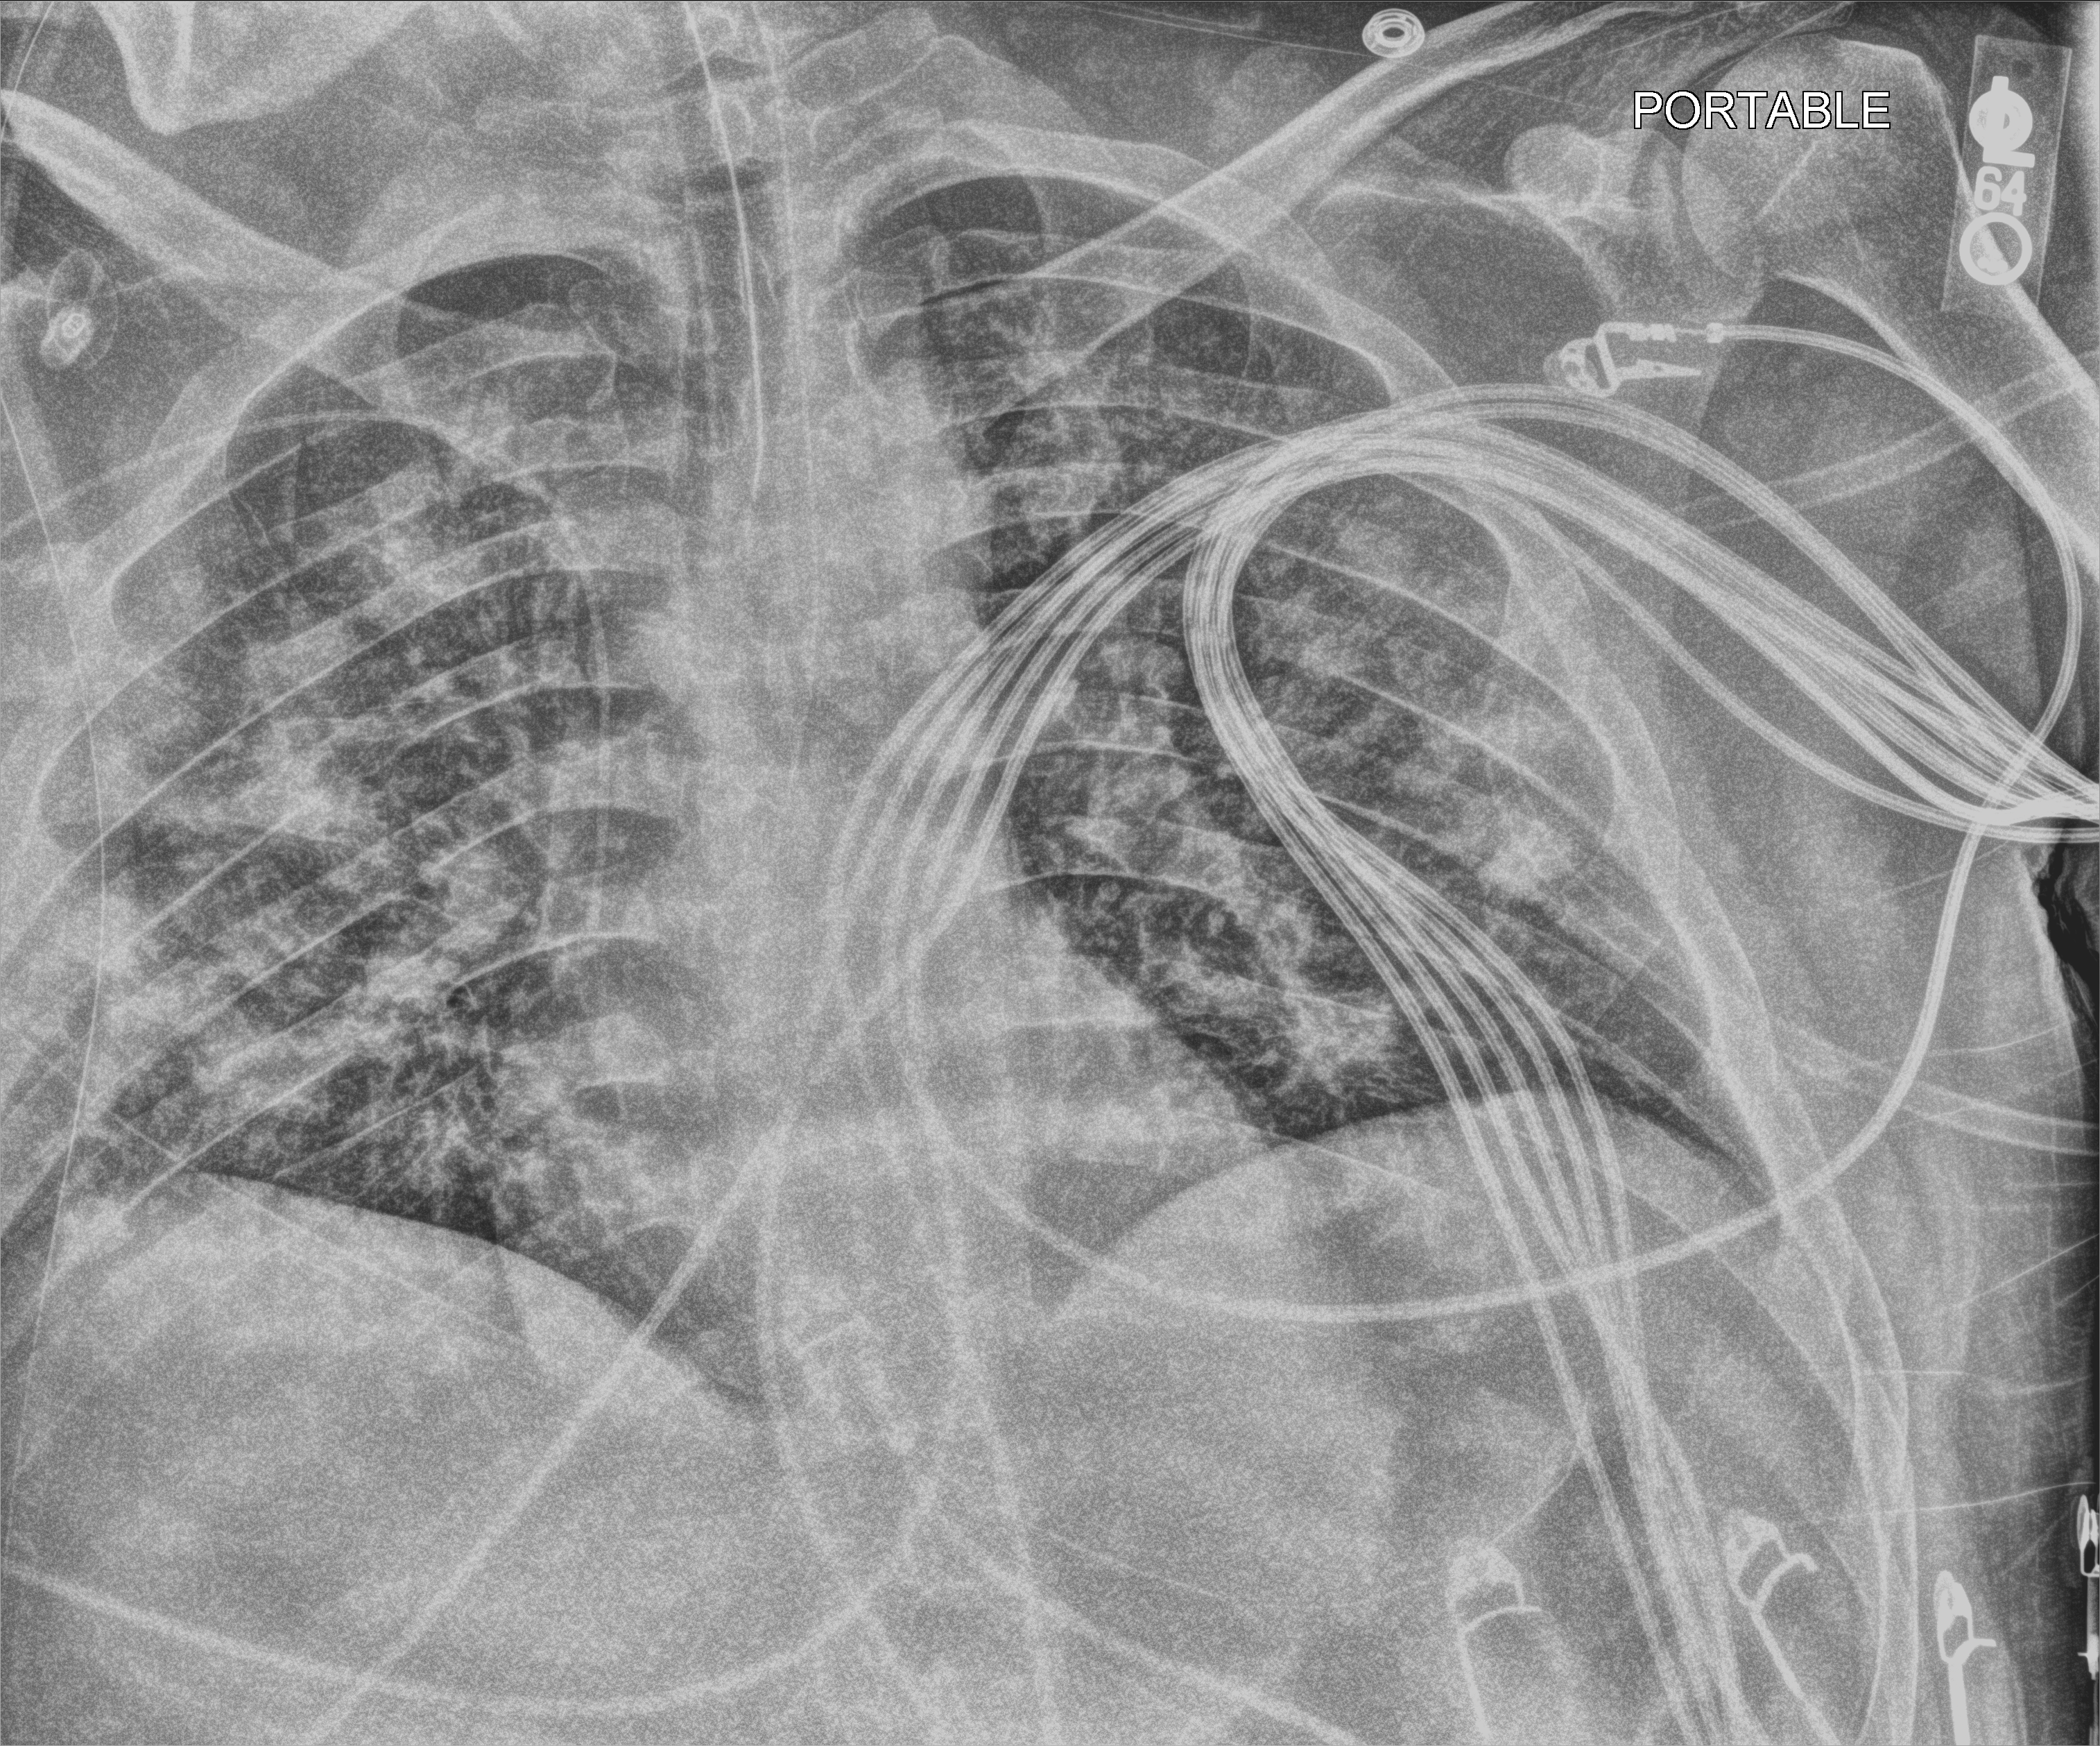
Bedside chest radiograph (computed radiography). Female patient hospitalised with COVID-19, age 18–59 years.
Admission-level facts for this patient (not findings on this image; timing relative to this image not recorded):
- mechanically ventilated during this hospital stay: yes